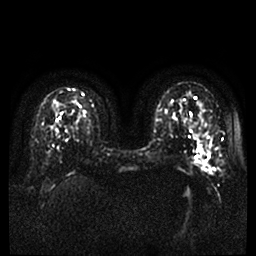
Breast MRI, one axial slice; diffusion-weighted series; image 2 of 4 stored at this slice position (different b-values; order by instance number); 1.5 T; 4 mm slice thickness; 256 × 256 image matrix. Female patient.
Structures marked on this image (manually delineated by an expert):
- tumour on diffusion-weighted imaging: bounding box <200,149,211,173> (left, top, right, bottom; pixels)